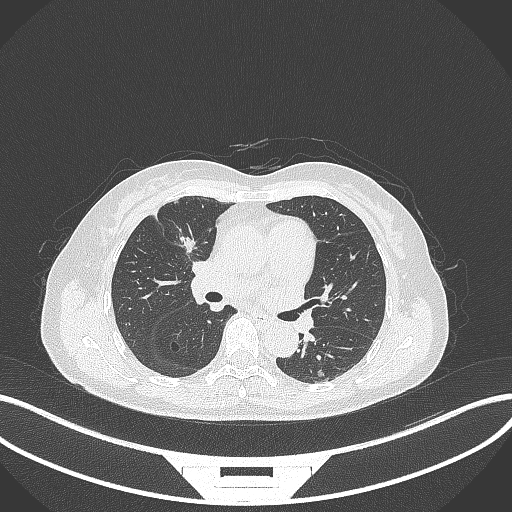
Chest CT, one axial slice. Slice 167 of 284 in the series (ordered by position). 120 kVp. Lung window (W 1500 / L -600 HU). 1 mm slice thickness. 512 × 512 image matrix, field of view 400 × 400 mm. Patient: female, 51 years. From the clinical record (not read from this slice): clinical TNM (as recorded): T1c N0 M0; histopathological grade: G2.
Structures marked on this image (bounding box drawn by a radiologist):
- lung tumour (recorded histology: adenocarcinoma): bounding box (x1, y1, x2, y2) in pixels: (179, 230, 205, 257)